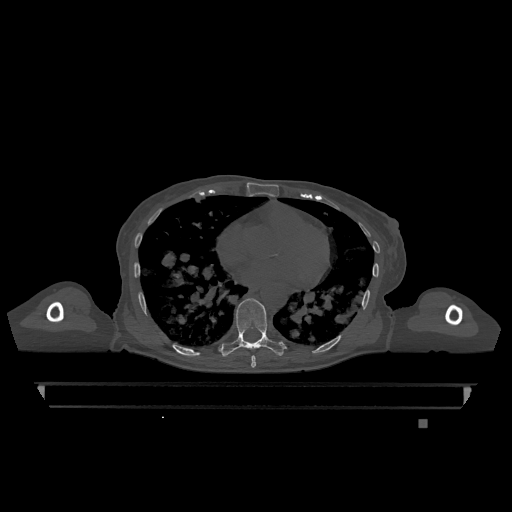
CT including the spine, one axial slice; slice 696 of 1317 in the series (ordered by position); bone window (W 1800 / L 400 HU); 0.5 mm slice thickness; 512 × 512 image matrix, field of view 500 × 500 mm. Female patient, age 74 years. From the clinical record (not read from this slice): primary cancer: lung; vertebrae with lytic lesions (as recorded): T1, T4, T5, T6, L4, L5.
Structures marked on this image (semi-automatic segmentation, software-assisted and operator-edited):
- T7 vertebra: bounding box (x1, y1, x2, y2) in pixels: (251, 355, 256, 368)
- T9 vertebra: (221, 298, 284, 357)